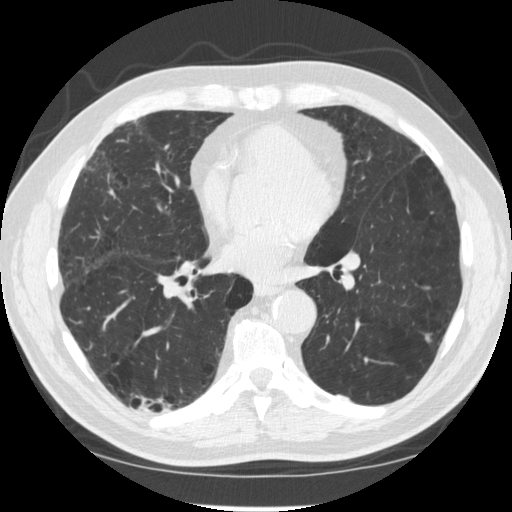
Axial slice from a low-dose chest CT screening exam. Second annual screen. Lung window (W 1500 / L -600 HU). Slice 154 of 303 in the series. Male, age 70 years at enrolment. Former smoker at enrolment.
- Expert-annotated lung lesion, bounding box (x1, y1, x2, y2) in pixels: (125, 376, 176, 431).
- The screening reader recorded 2 non-calcified nodules or masses ≥4 mm on this exam (right lower lobe, right lower lobe); which of them this box marks is not recorded.
- Official screen result: negative screen, significant abnormalities not suspicious for lung cancer.
- Lung cancer was diagnosed 617 days after this screen: squamous cell carcinoma, NOS, right upper lobe, poorly differentiated (G3), stage IV (AJCC 6th edition).